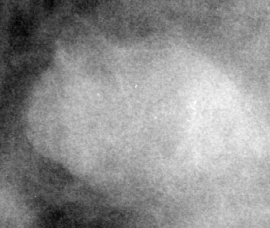
Cropped region of a digitized screen-film mammogram centred on a radiologist-marked abnormality, right breast, MLO view.
Finding: mass, shape oval, margins circumscribed; BI-RADS assessment category 4; pathology (as recorded): benign.